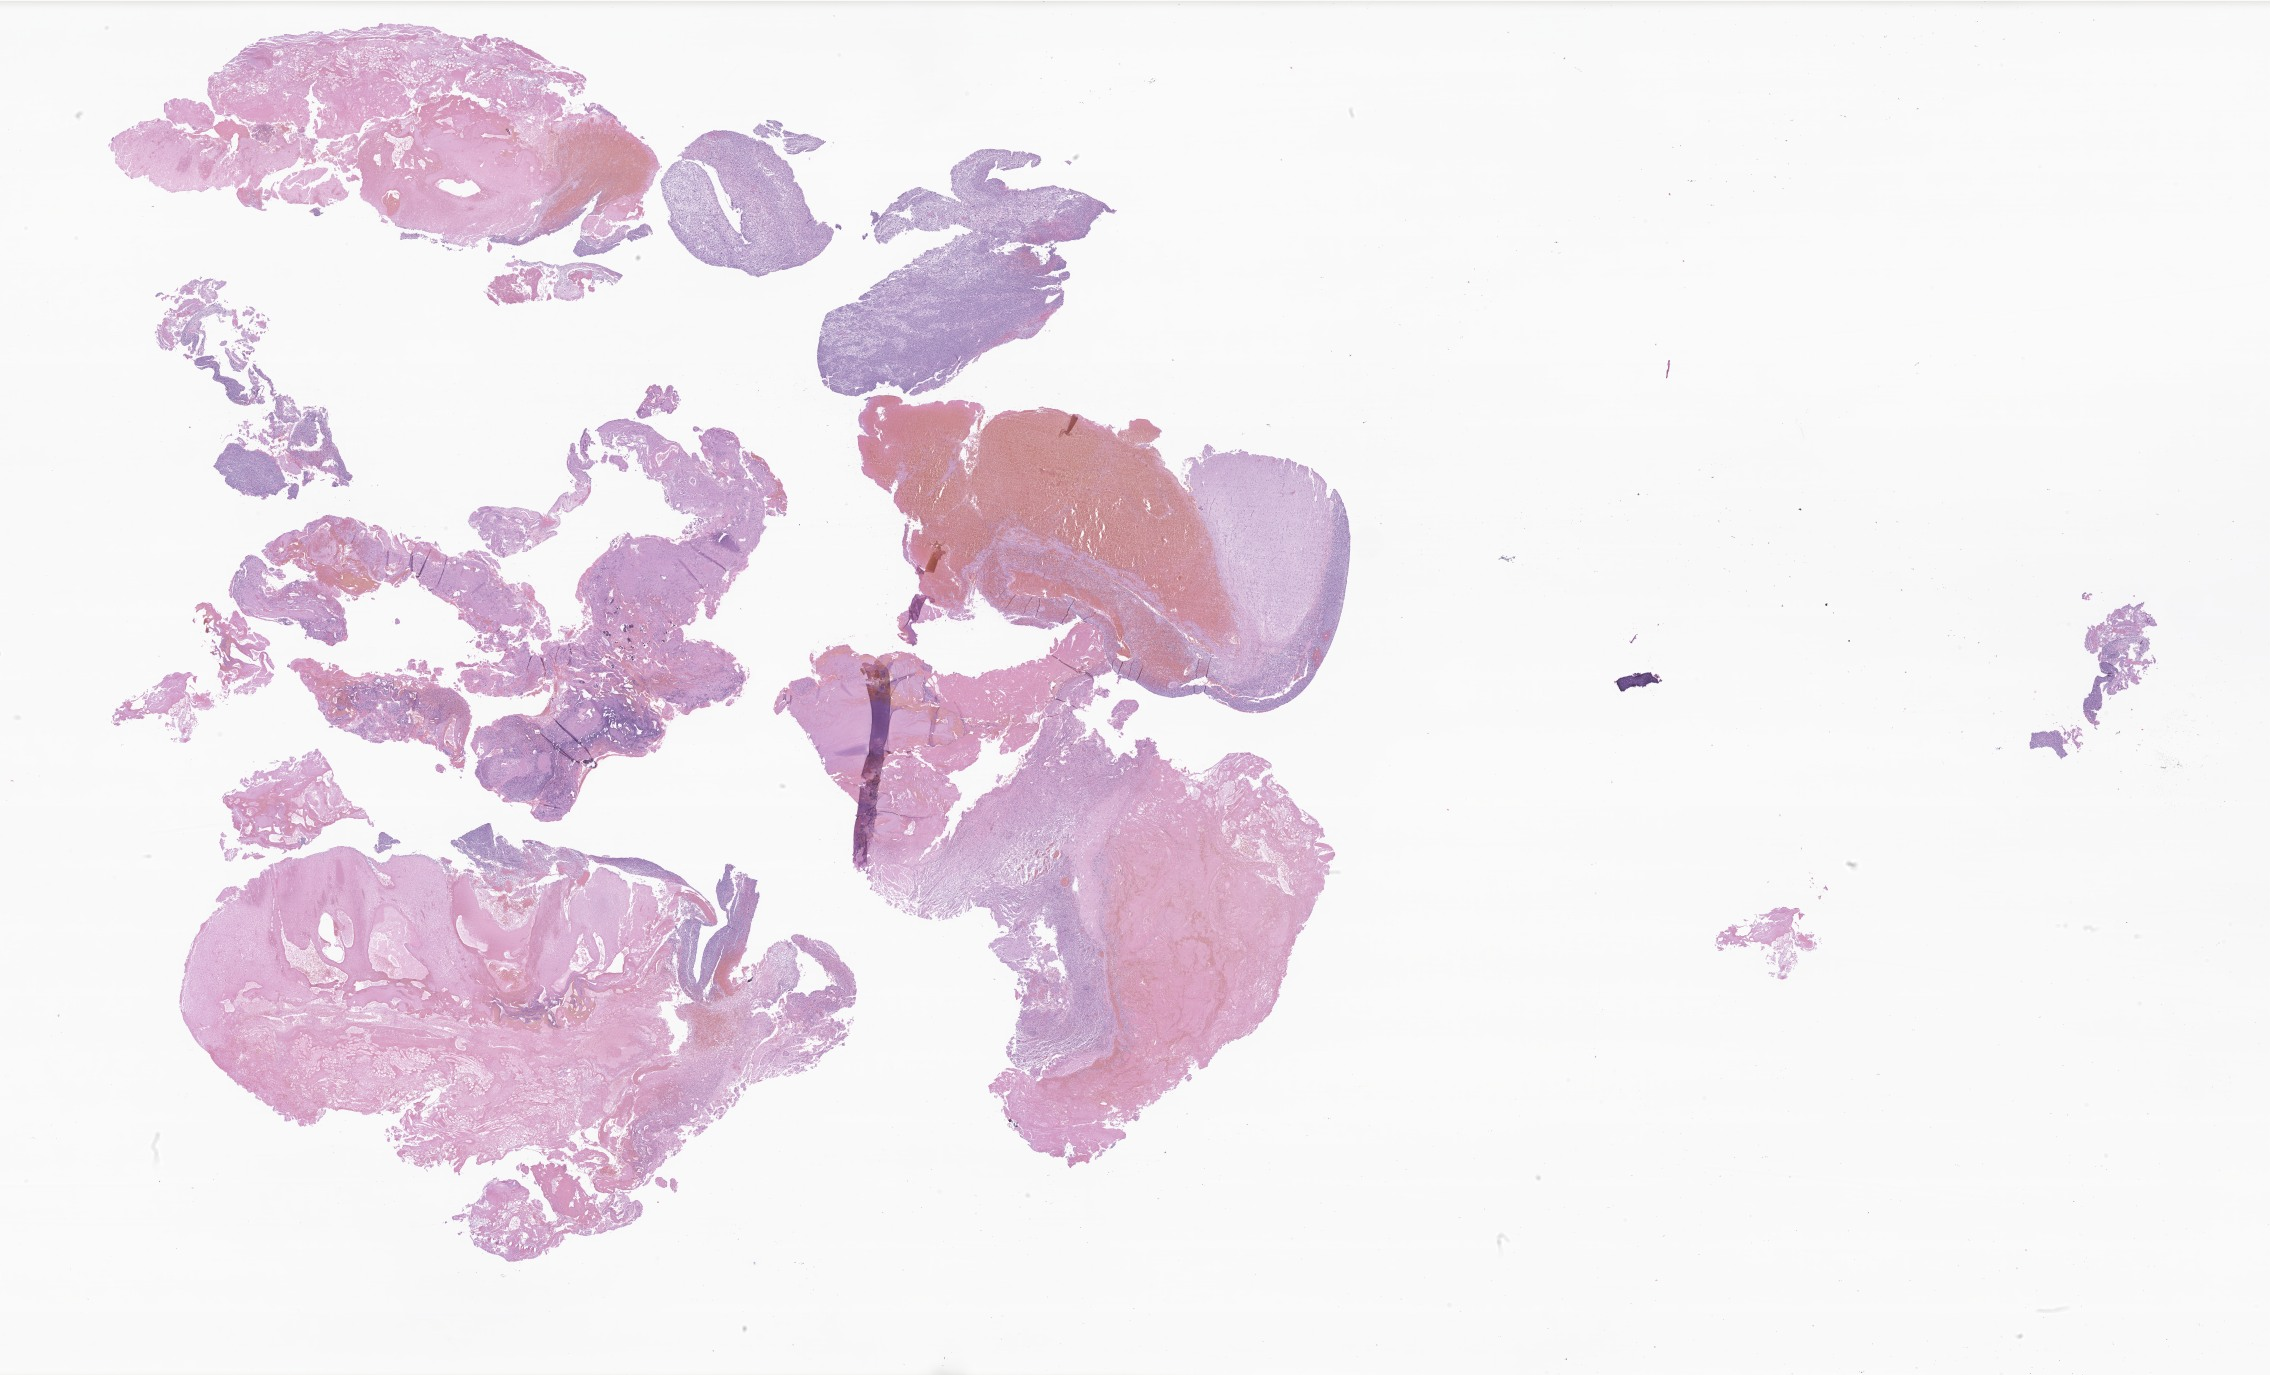
Whole-slide image, haematoxylin and eosin stain of tumor tissue from the temporal lobe — low-resolution overview of the scanned area, about 38.3 x 23.2 mm, formalin-fixed paraffin-embedded section. Patient male; age 106 months (8 years 10 months).
Diagnosis (ICD-O-3 morphology term): Sarcoma, NOS.